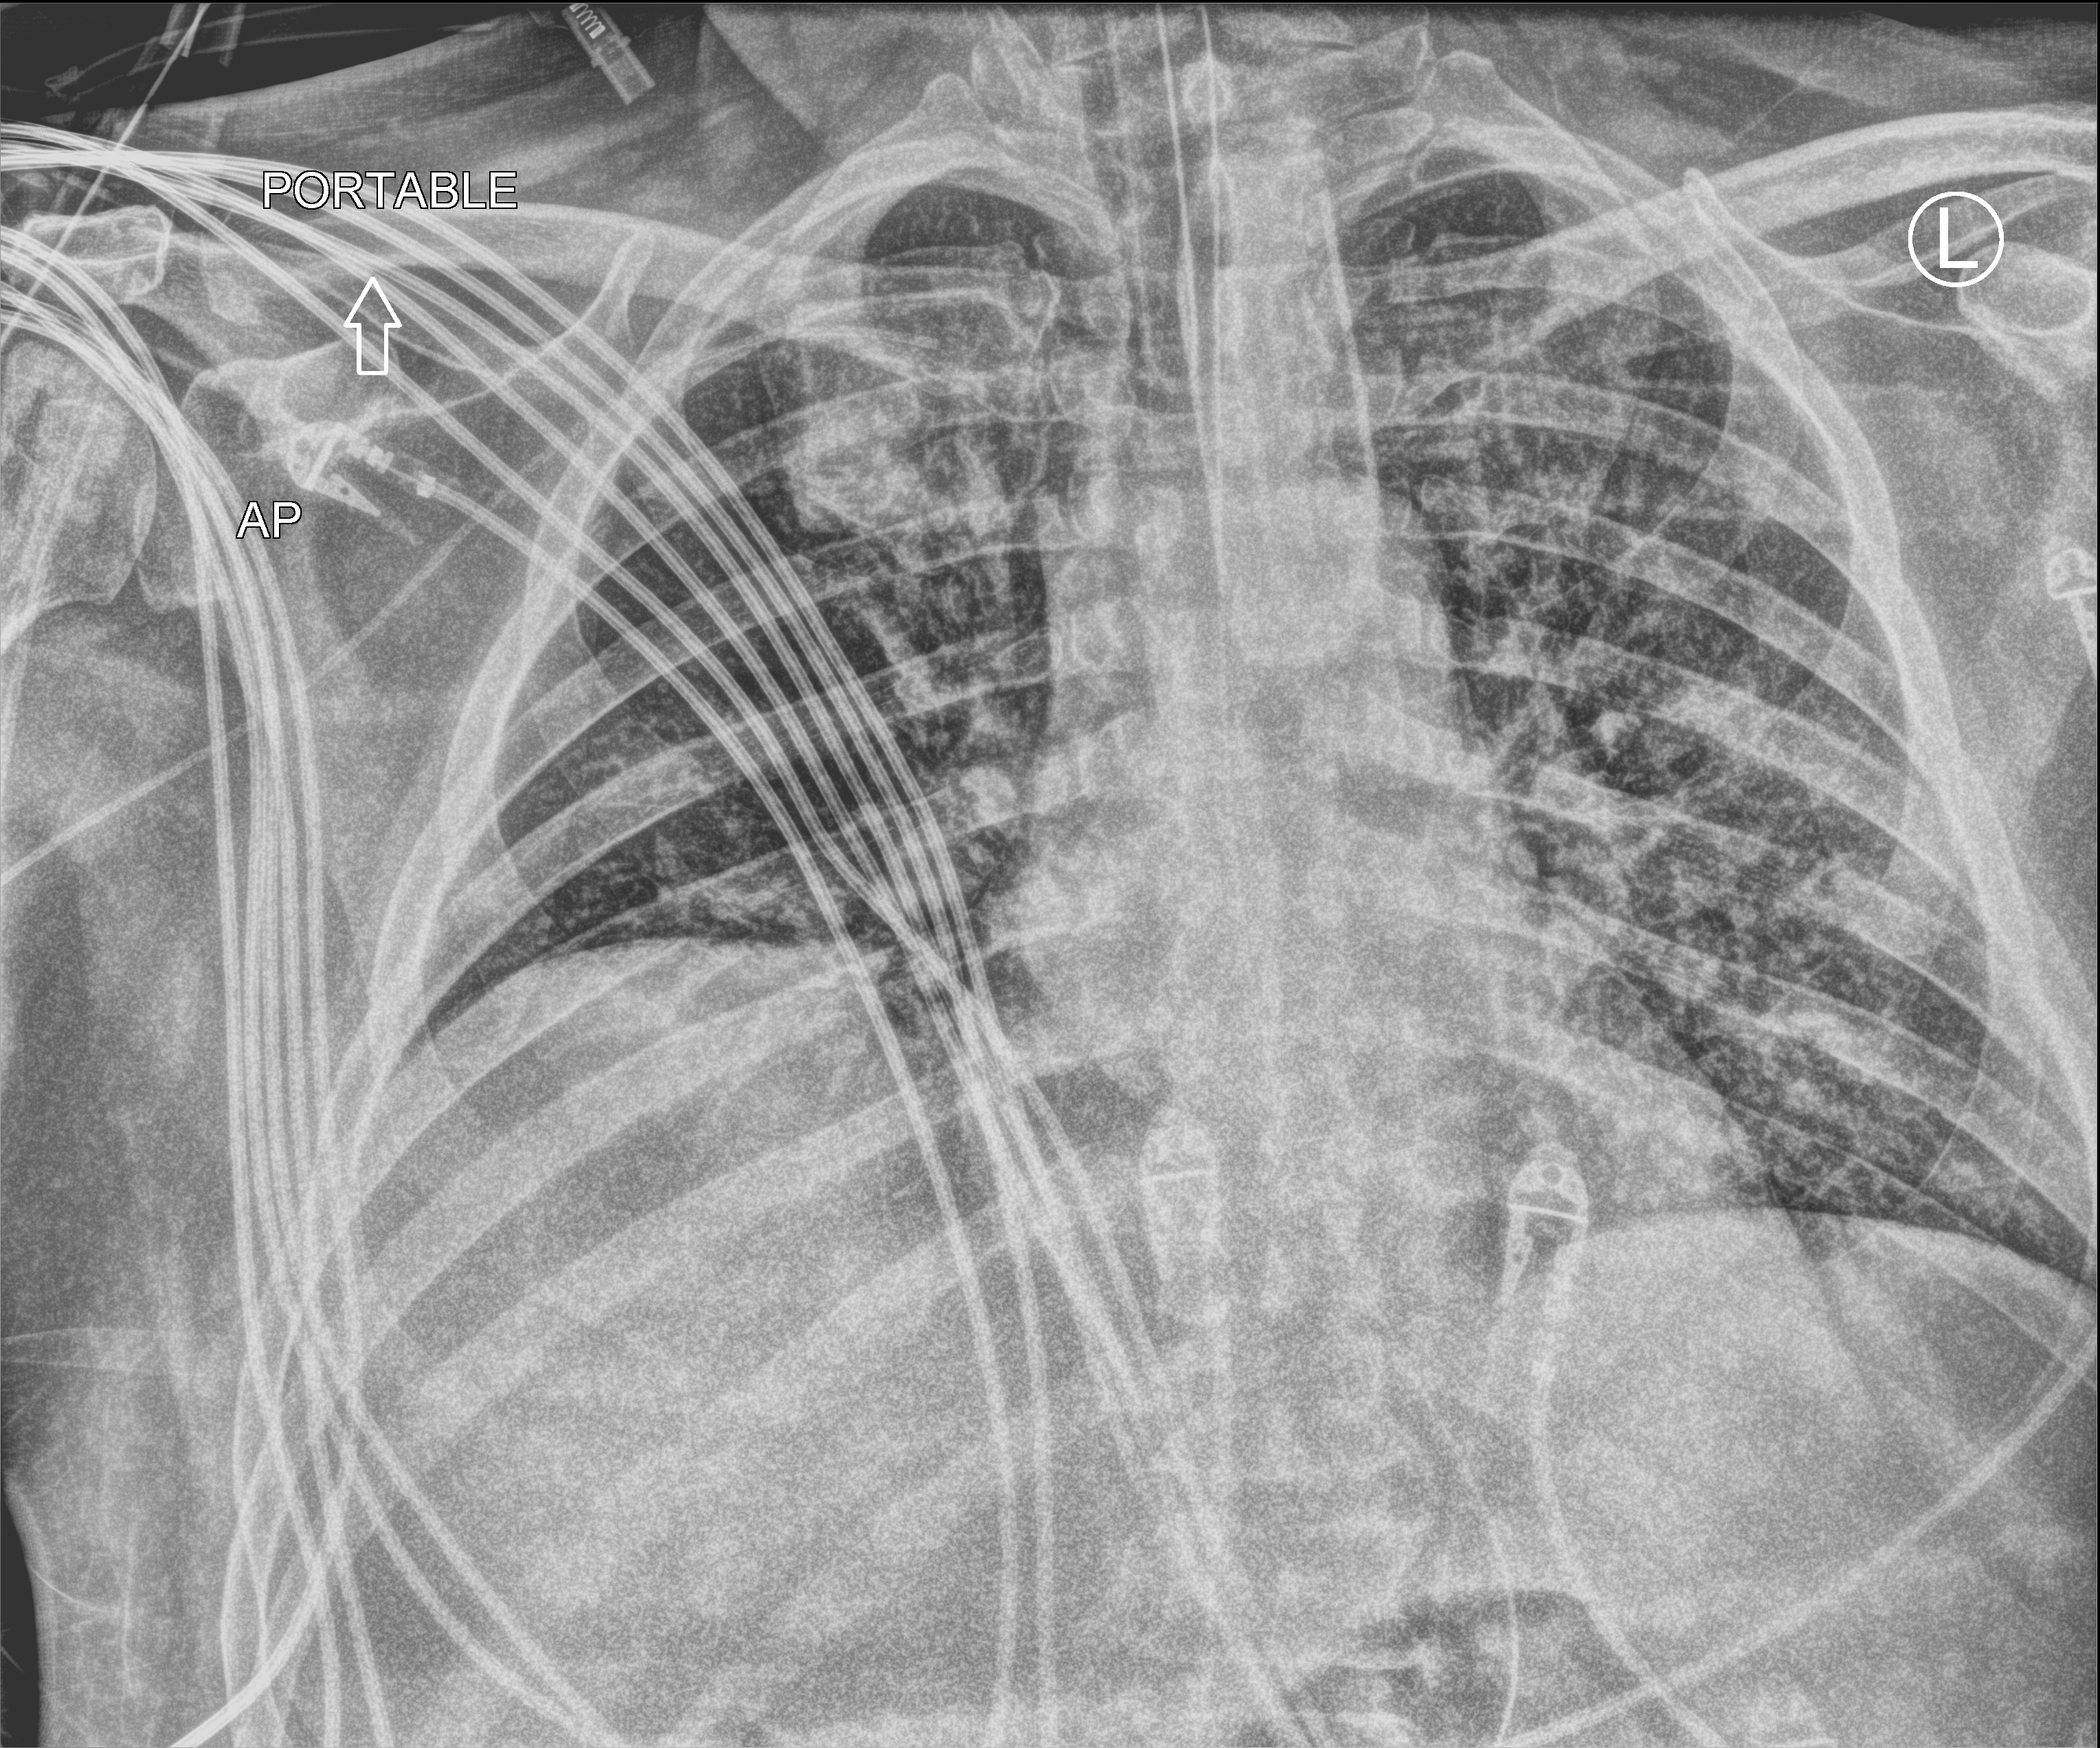
Bedside chest radiograph (computed radiography). Patient hospitalised with COVID-19; male, aged 18–59 years.
Admission-level facts for this patient (not findings on this image; timing relative to this image not recorded): mechanically ventilated during this hospital stay: yes; smoking status (admission record): never.